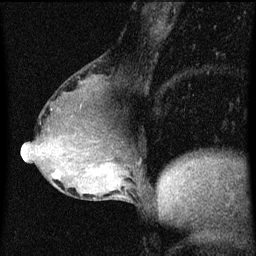
Breast MRI (dynamic contrast-enhanced), one sagittal slice; position 31 of 60 along the scan axis; dynamic contrast-enhanced series, image 2 of 3 at this slice position (ordered by acquisition); 1.5 T; TE 4.2 ms, TR 8 ms; 2 mm slice thickness; 256 × 256 image matrix, field of view 180 × 180 mm. Patient: female, 49 years.
Outlined on this slice (semi-automatically segmented with operator editing):
- analysis volume of interest (the breast-tissue region the enhancement analysis was run in; not a lesion): box from (x=51, y=158) to (x=96, y=185) px
- tumour enhancement mask (voxels above the 70 % enhancement threshold inside the analysis volume of interest): (x=53, y=170)–(x=62, y=179)